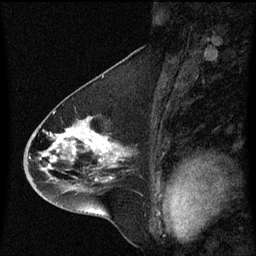
Breast MRI (dynamic contrast-enhanced), one sagittal slice. Slice 32 of 60 in the series (ordered by position). Dynamic contrast-enhanced series, image 2 of 3 at this slice position (ordered by acquisition). 1.5 T. TE 4.2 ms, TR 8.4 ms. 2 mm slice thickness. 256 × 256 image matrix, field of view 200 × 200 mm. Female patient, age 46 years. From the clinical record (not read from this slice): setting: breast cancer imaged before/during neoadjuvant chemotherapy; receptor status: HER2-positive.
Structures marked on this image (semi-automatic segmentation, software-assisted and operator-edited):
- analysis volume of interest (the breast-tissue region the enhancement analysis was run in; not a lesion): bounding box <24,112,133,195> (left, top, right, bottom; pixels)
- tumour enhancement mask (voxels above the 70 % enhancement threshold inside the analysis volume of interest): <45,132,118,183>